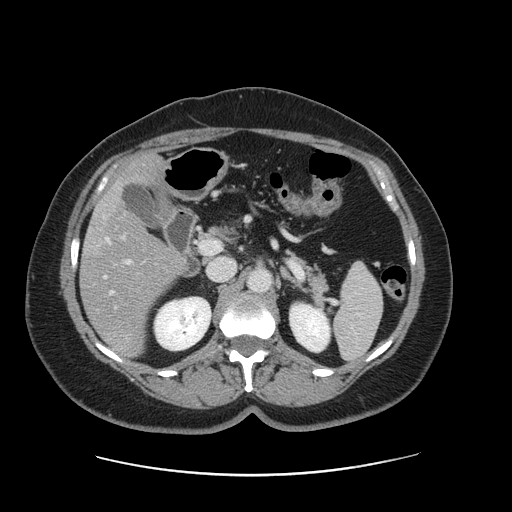
Contrast-enhanced abdominal CT, one axial slice; slice 76 of 161 in the series (ordered by position); soft-tissue window (W 400 / L 40 HU); 2.5 mm slice thickness; 512 × 512 image matrix, field of view 398 × 398 mm. Female patient, age 62 years. Case-level facts recorded for this patient, not image findings: diagnosis: colorectal cancer liver metastases, imaged before liver resection; multiple liver metastases: no; largest metastasis: 2.5 cm; disease in both lobes: no.
Outlined on this slice (manually delineated by an expert):
- hepatic veins: box from (x=105, y=238) to (x=114, y=294) px
- liver: (x=82, y=156)–(x=183, y=358)
- planned liver remnant (the part of the liver to remain after resection): (x=116, y=157)–(x=161, y=189)
- portal vein (with intrahepatic branches): (x=121, y=235)–(x=131, y=264)